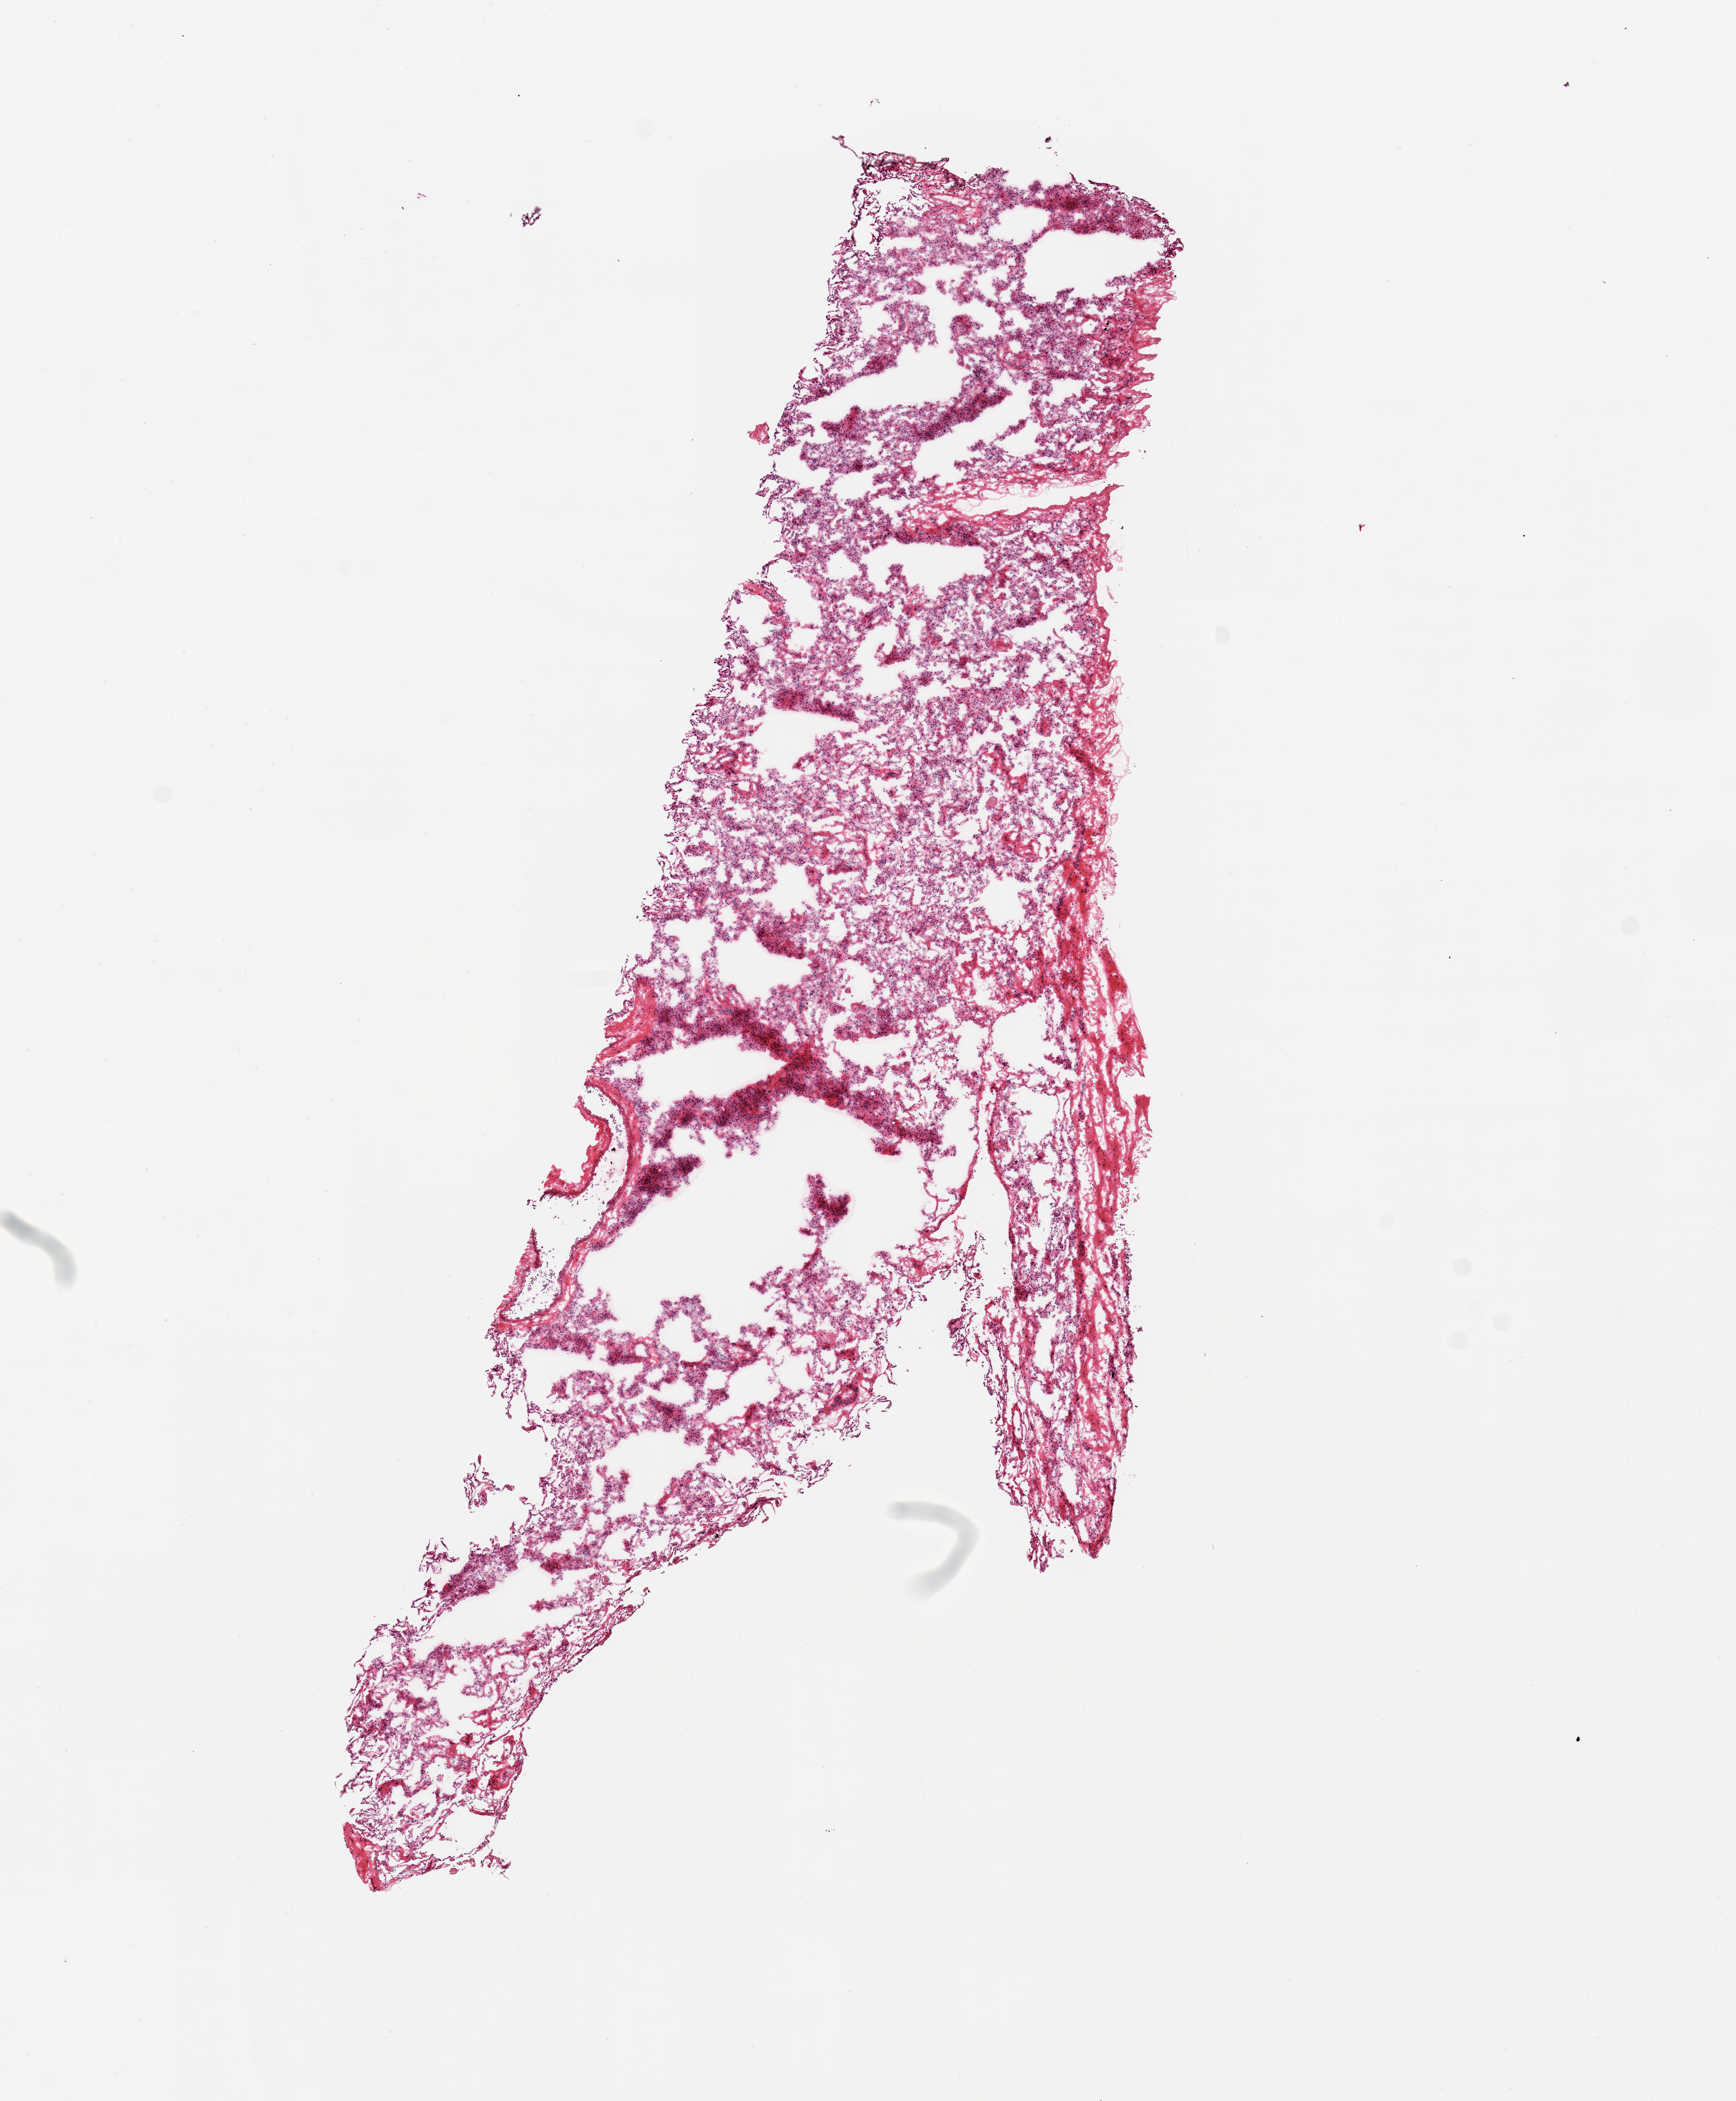
Hematoxylin and eosin (H&E) whole-slide image — a low-resolution overview of the entire scanned area, about 9.8 x 11.9 mm (acquisition: 20x scan), frozen section, section of lung (target tissue), tissue donor sample. Donor: male.
Review note (as recorded): 1 piece.